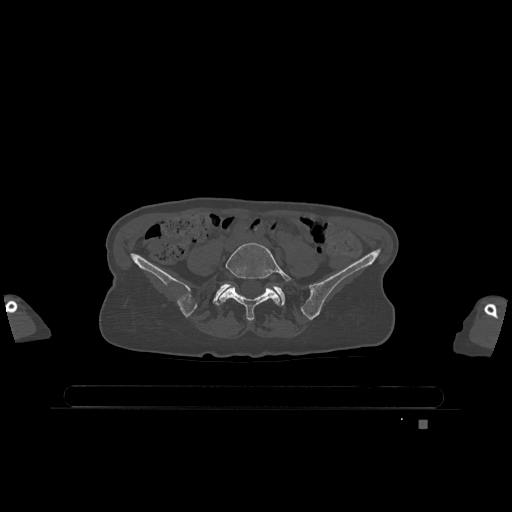
CT including the spine, one axial slice; slice 233 of 1317 in the series (ordered by position); bone window (W 1800 / L 400 HU); 0.5 mm slice thickness; 512 × 512 image matrix, field of view 500 × 500 mm. Female patient, age 74 years. From the clinical record (not read from this slice): primary cancer: lung; vertebrae with lytic lesions (as recorded): T1, T4, T5, T6, L4, L5.
Structures marked on this image (semi-automatically segmented with operator editing):
- L5 vertebra: bounding box <217,243,292,321> (left, top, right, bottom; pixels)